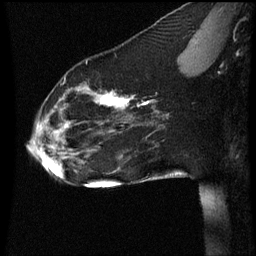
Breast MRI (dynamic contrast-enhanced), one sagittal slice; position 20 of 60 along the scan axis; dynamic contrast-enhanced series, image 2 of 3 at this slice position (ordered by acquisition); 1.5 T; TE 4.2 ms, TR 8.9 ms; 2 mm slice thickness; 256 × 256 image matrix, field of view 200 × 200 mm. Female patient, age 35 years. From the clinical record (not read from this slice): setting: breast cancer imaged before/during neoadjuvant chemotherapy; receptor status: HER2-positive.
Outlined on this slice (semi-automatically segmented with operator editing):
- analysis volume of interest (the breast-tissue region the enhancement analysis was run in; not a lesion): box from (x=26, y=66) to (x=177, y=177) px
- tumour enhancement mask (voxels above the 70 % enhancement threshold inside the analysis volume of interest): (x=48, y=92)–(x=157, y=131)